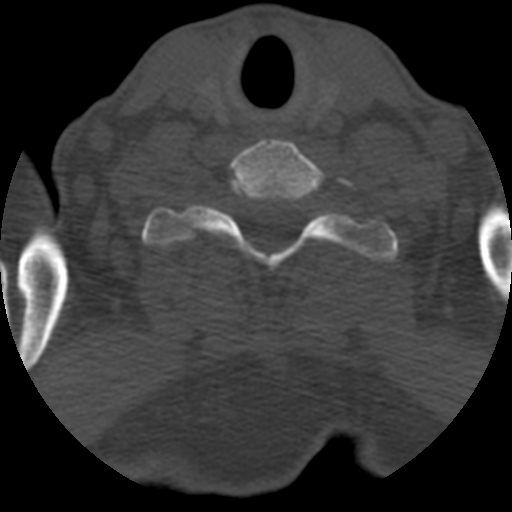
CT including the spine, one axial slice. Slice 525 of 708 in the series (ordered by position). One of 3 acquisitions stored at this slice position. Bone window (W 1800 / L 400 HU). 512 × 512 image matrix. Patient age 55 years. Case-level facts recorded for this patient, not image findings: primary cancer: colon; vertebrae with lytic lesions (as recorded): T12, L1, L5.
Structures marked on this image (semi-automatic segmentation, software-assisted and operator-edited):
- T1 vertebra: box from (x=141, y=186) to (x=397, y=272) px